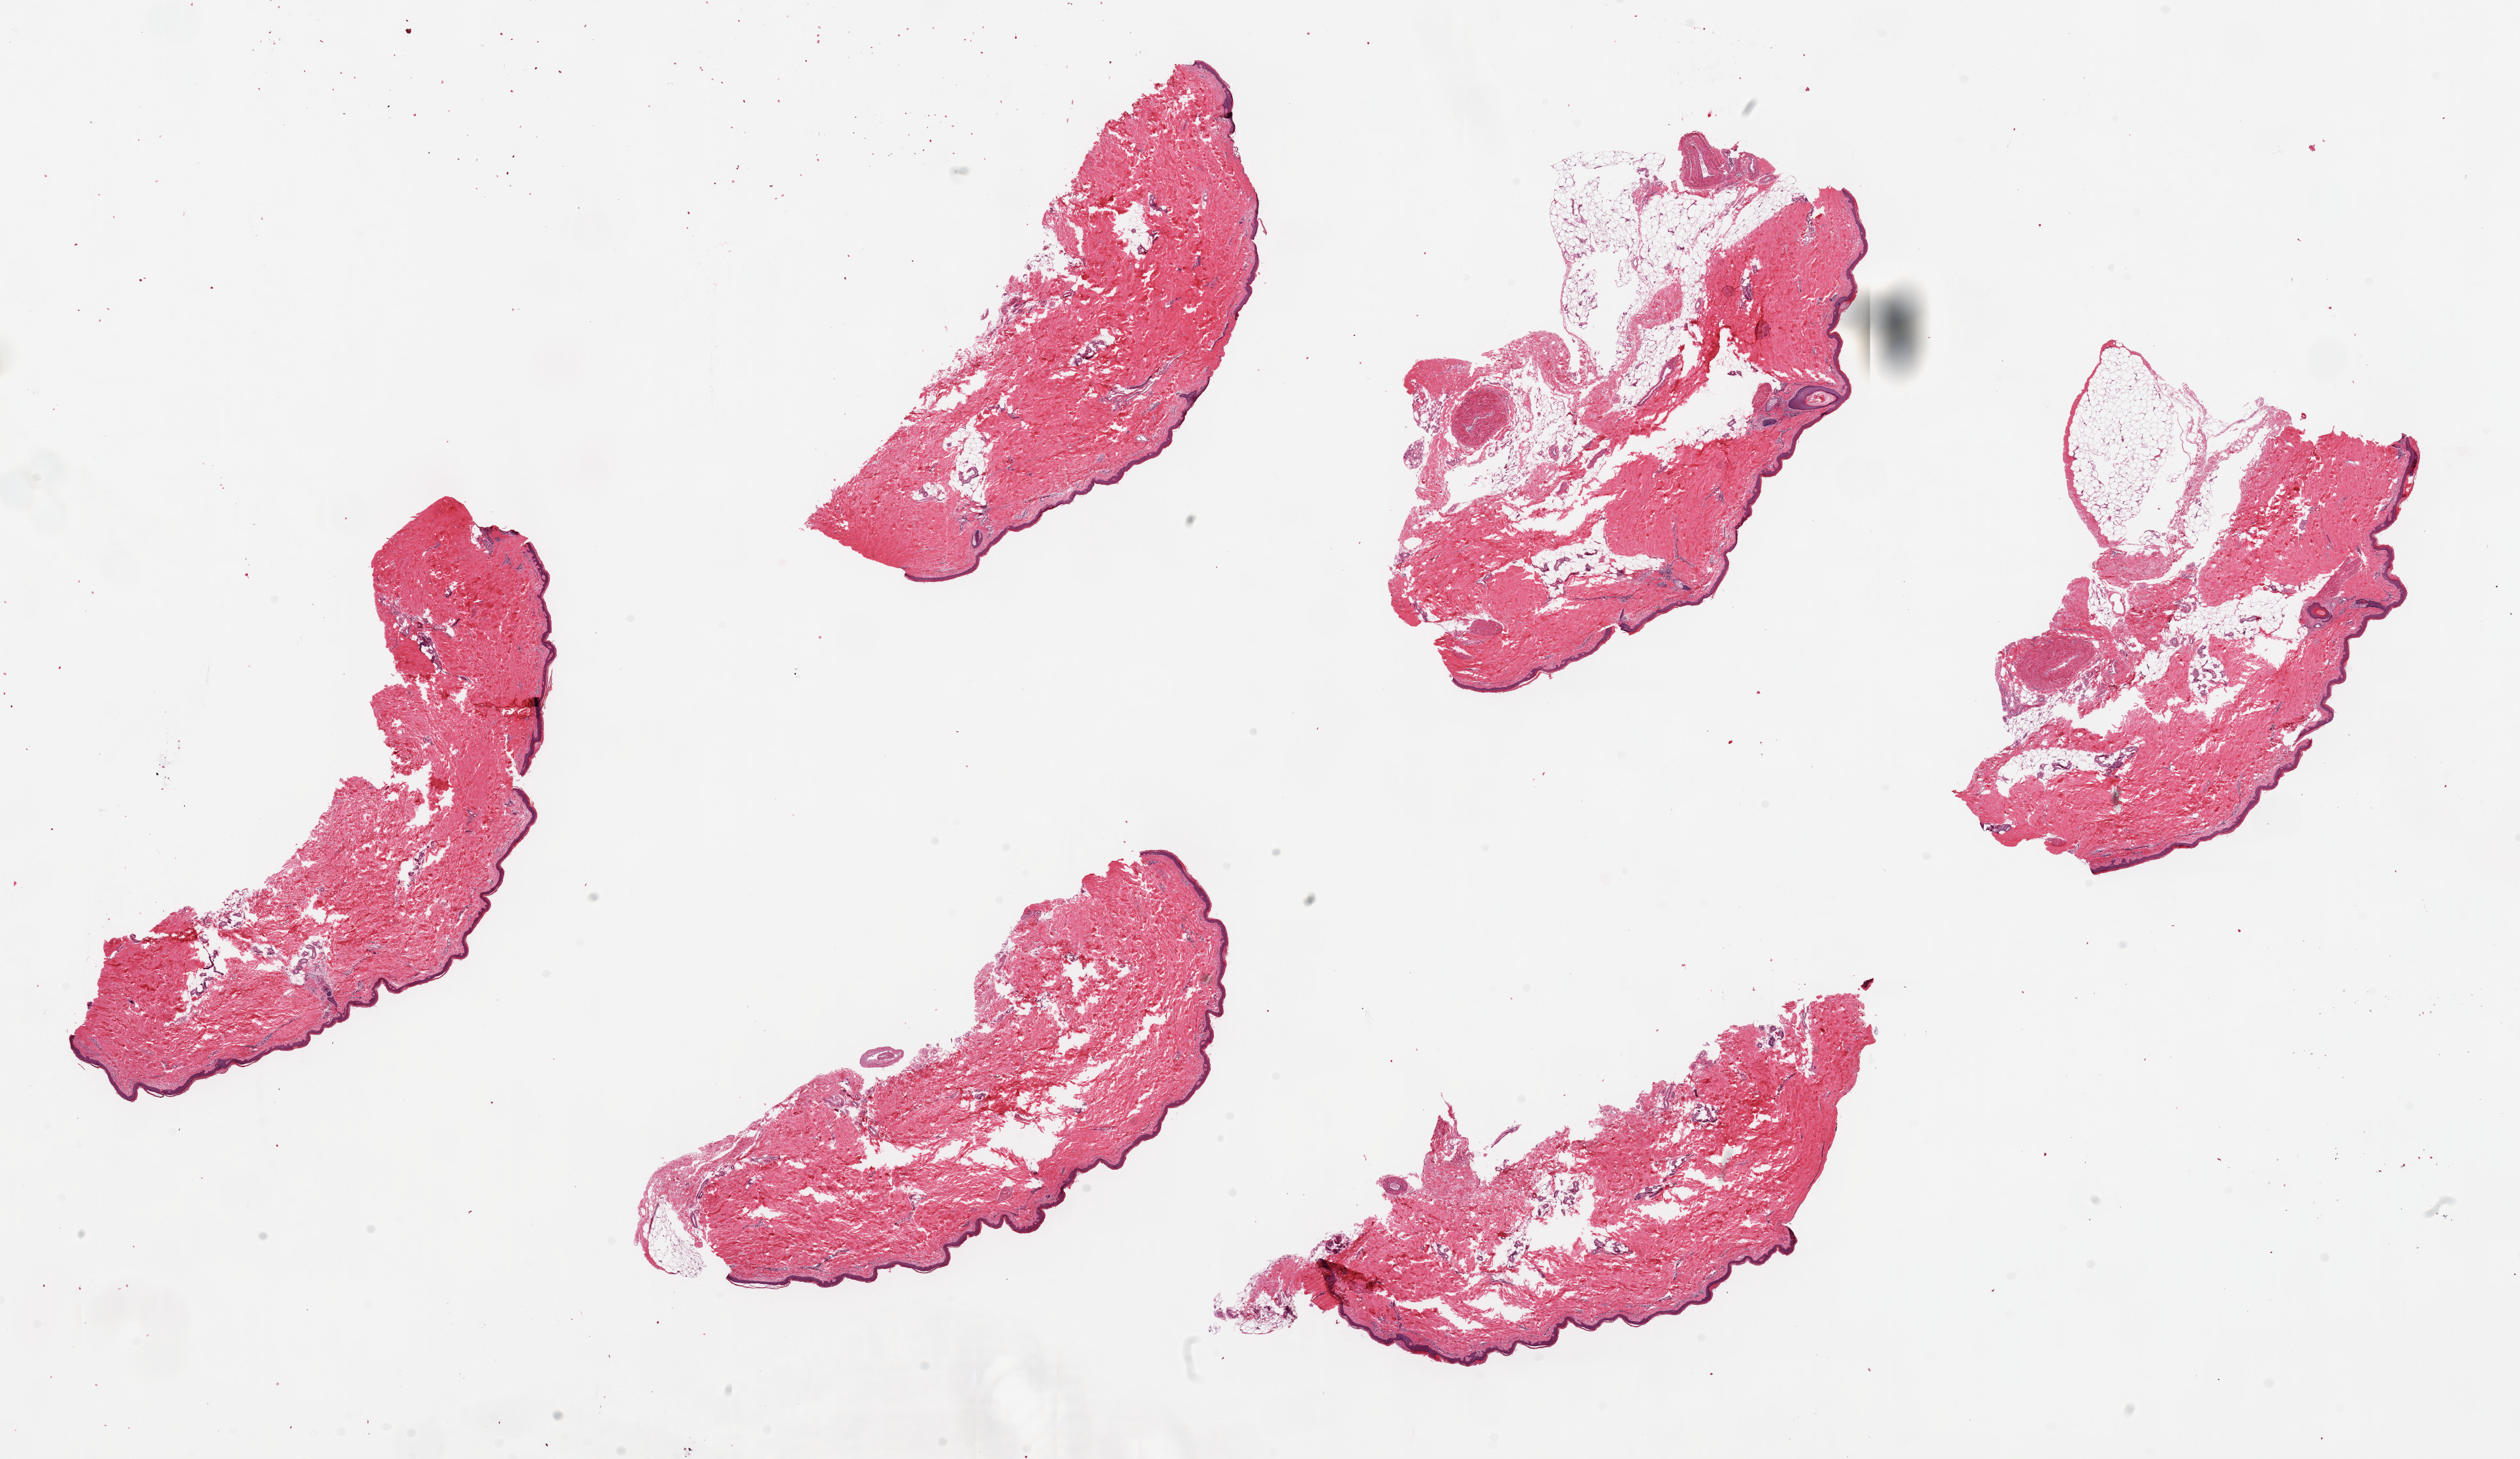
Digitized H&E-stained section — whole scanned area (about 30.5 x 17.7 mm, acquisition: 20x scan) shown as a low-resolution overview, PAXgene-fixed paraffin-embedded (PFPE) section, sampled site (target tissue): skin of lower leg, donor tissue sample.
• review note (as recorded): 6 ~7x2mm pieces; squamous epithelium is ~ 2-3% of specimen thickness